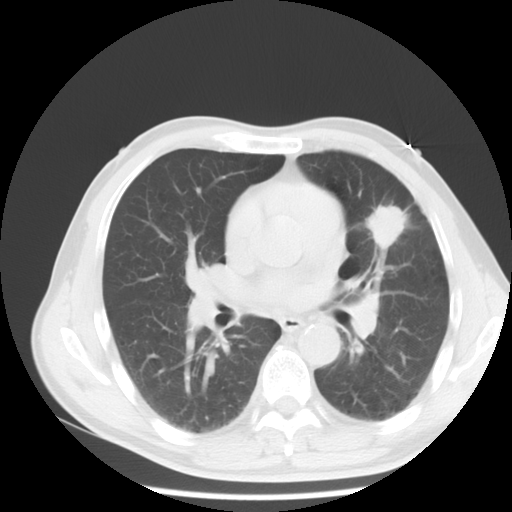
Chest CT, one axial slice; position 8 of 13 along the scan axis; reconstruction kernel STANDARD; lung window (W 1500 / L -600 HU); 512 × 512 image matrix. Patient: male, 54 years. From the clinical record (not read from this slice): clinical TNM (as recorded): T1c N0 M0.
Structures marked on this image (rectangle marked by the reading radiologist):
- lung tumour (recorded histology: adenocarcinoma): box from (x=362, y=196) to (x=414, y=262) px